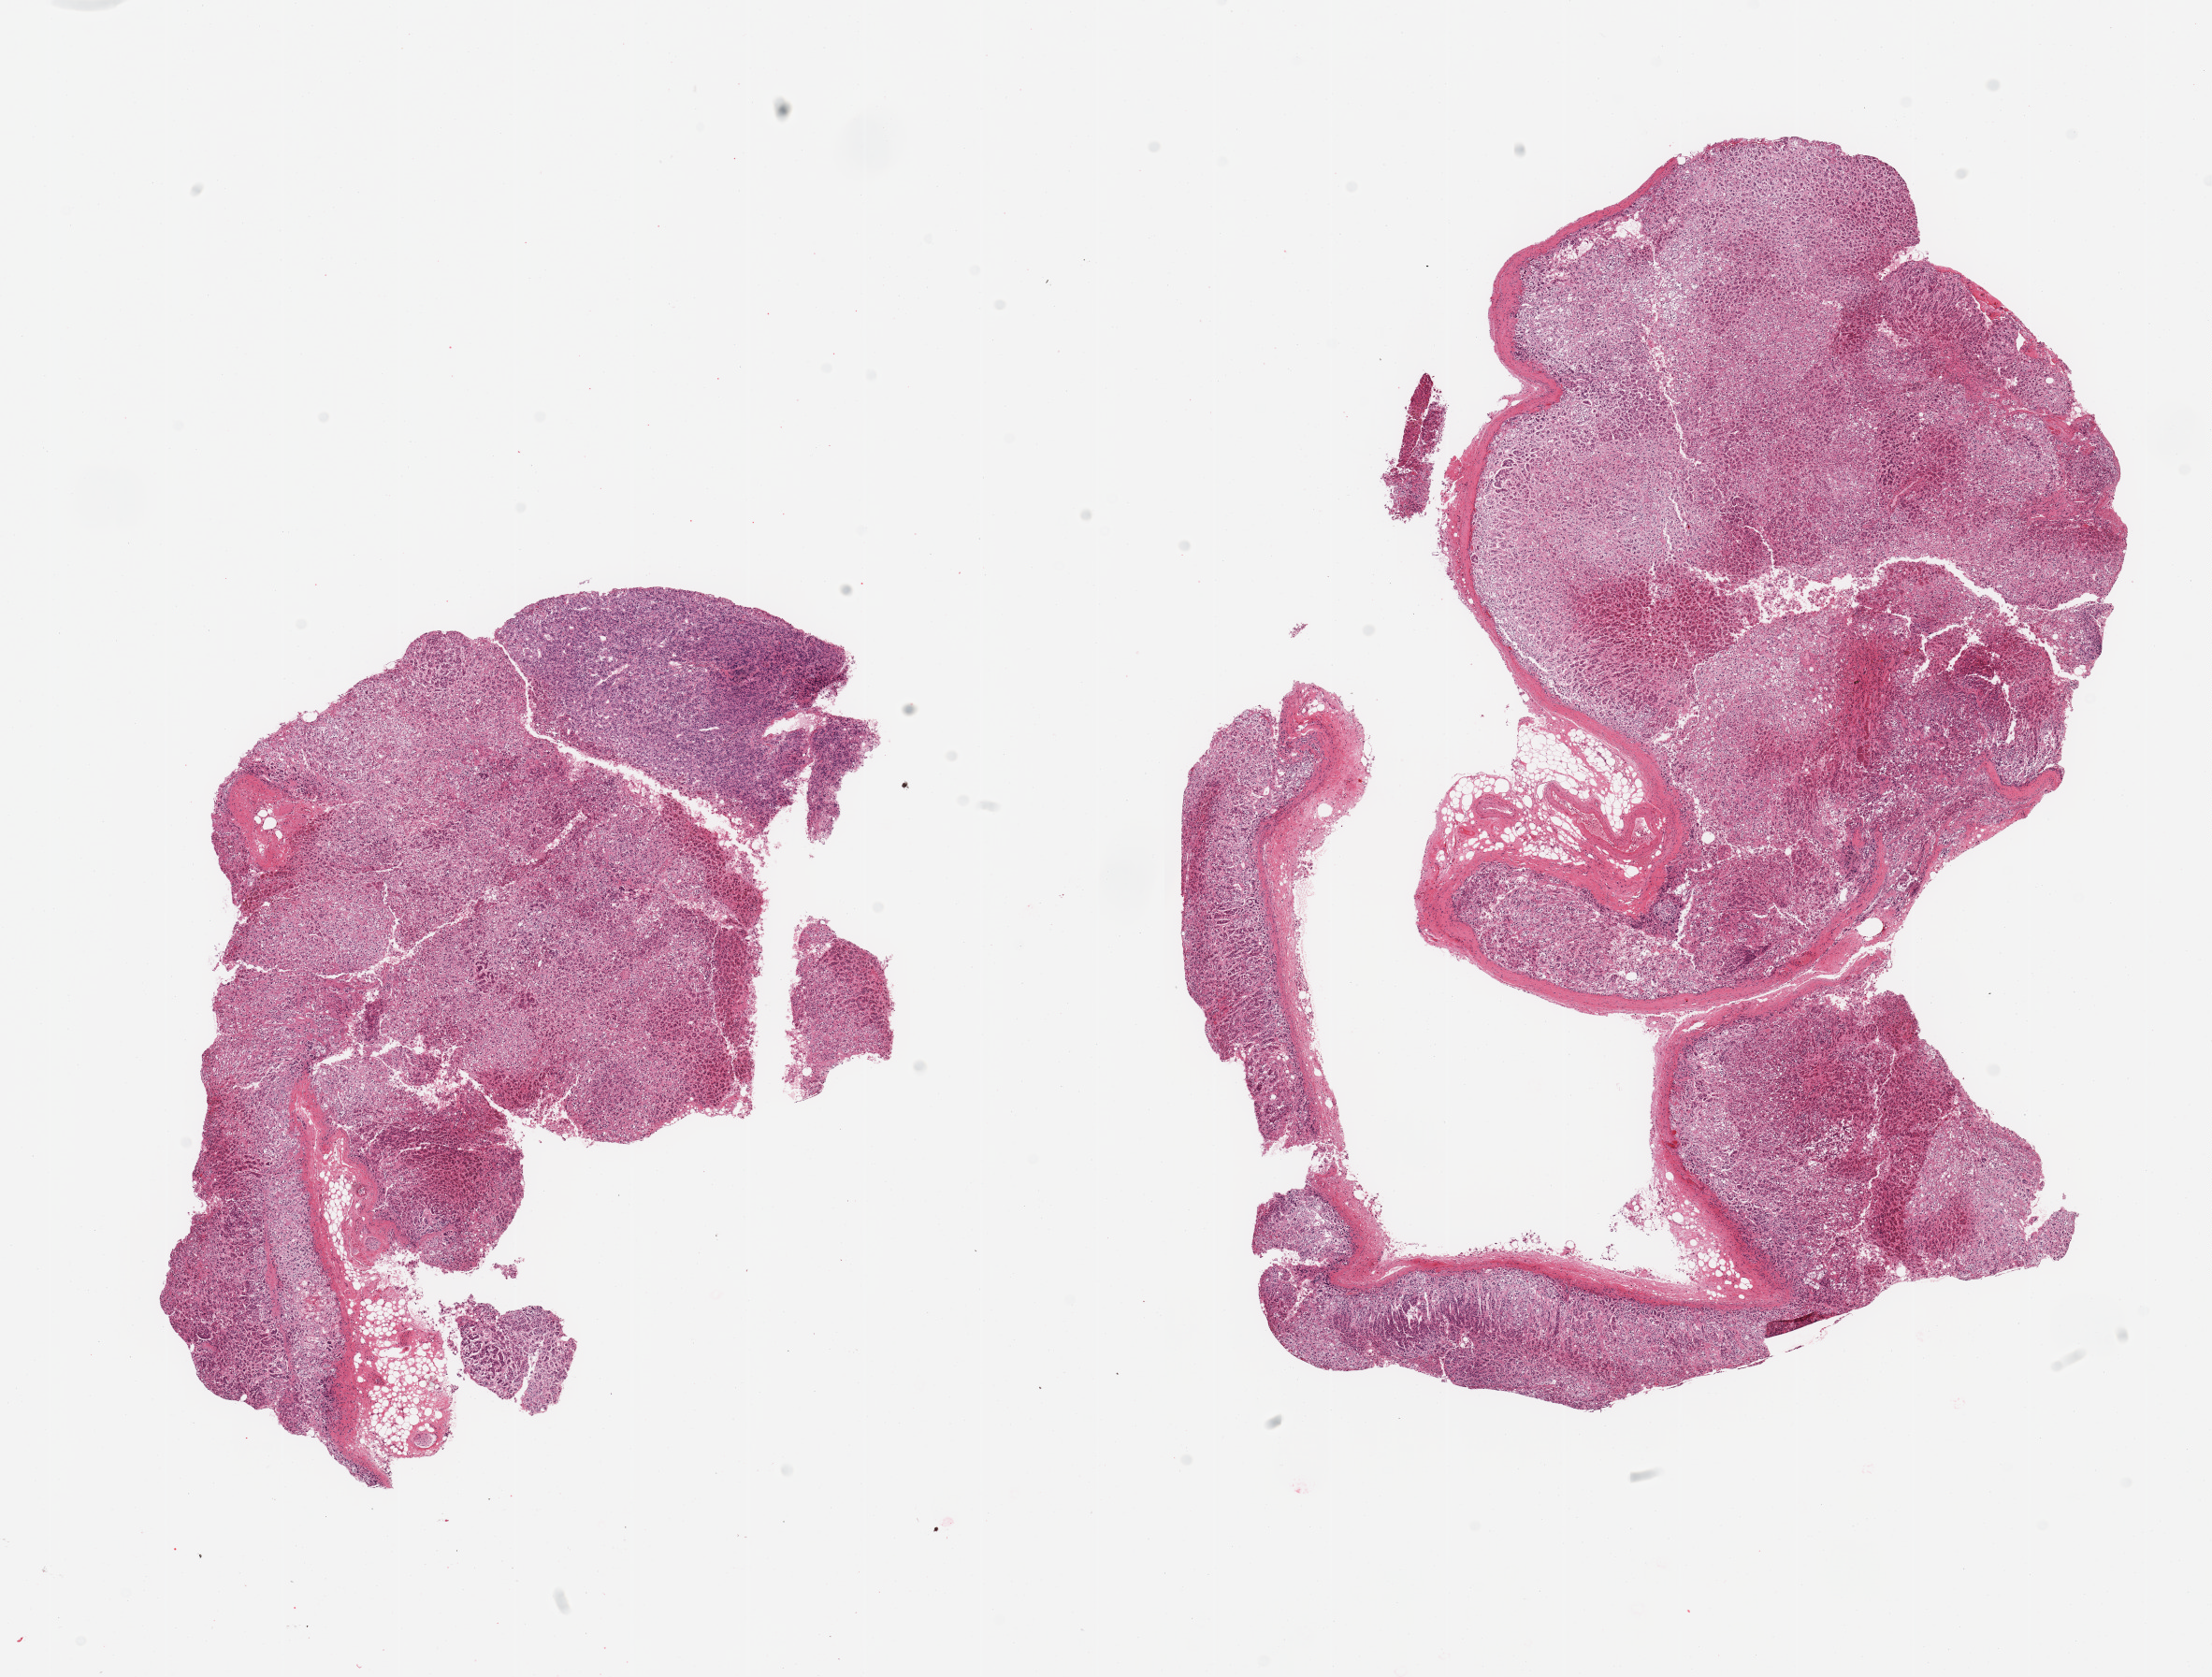
Digitized haematoxylin and eosin-stained section, brightfield, whole scanned area (about 18.7 x 14.2 mm) shown as a low-resolution overview. PAXgene-fixed paraffin-embedded (PFPE) section. Sampled site (target tissue): adrenal gland. Donor tissue sample. Donor: male.
Reviewer comment on this tissue sample: 2 pieces, cortex, minimal adherent fat.